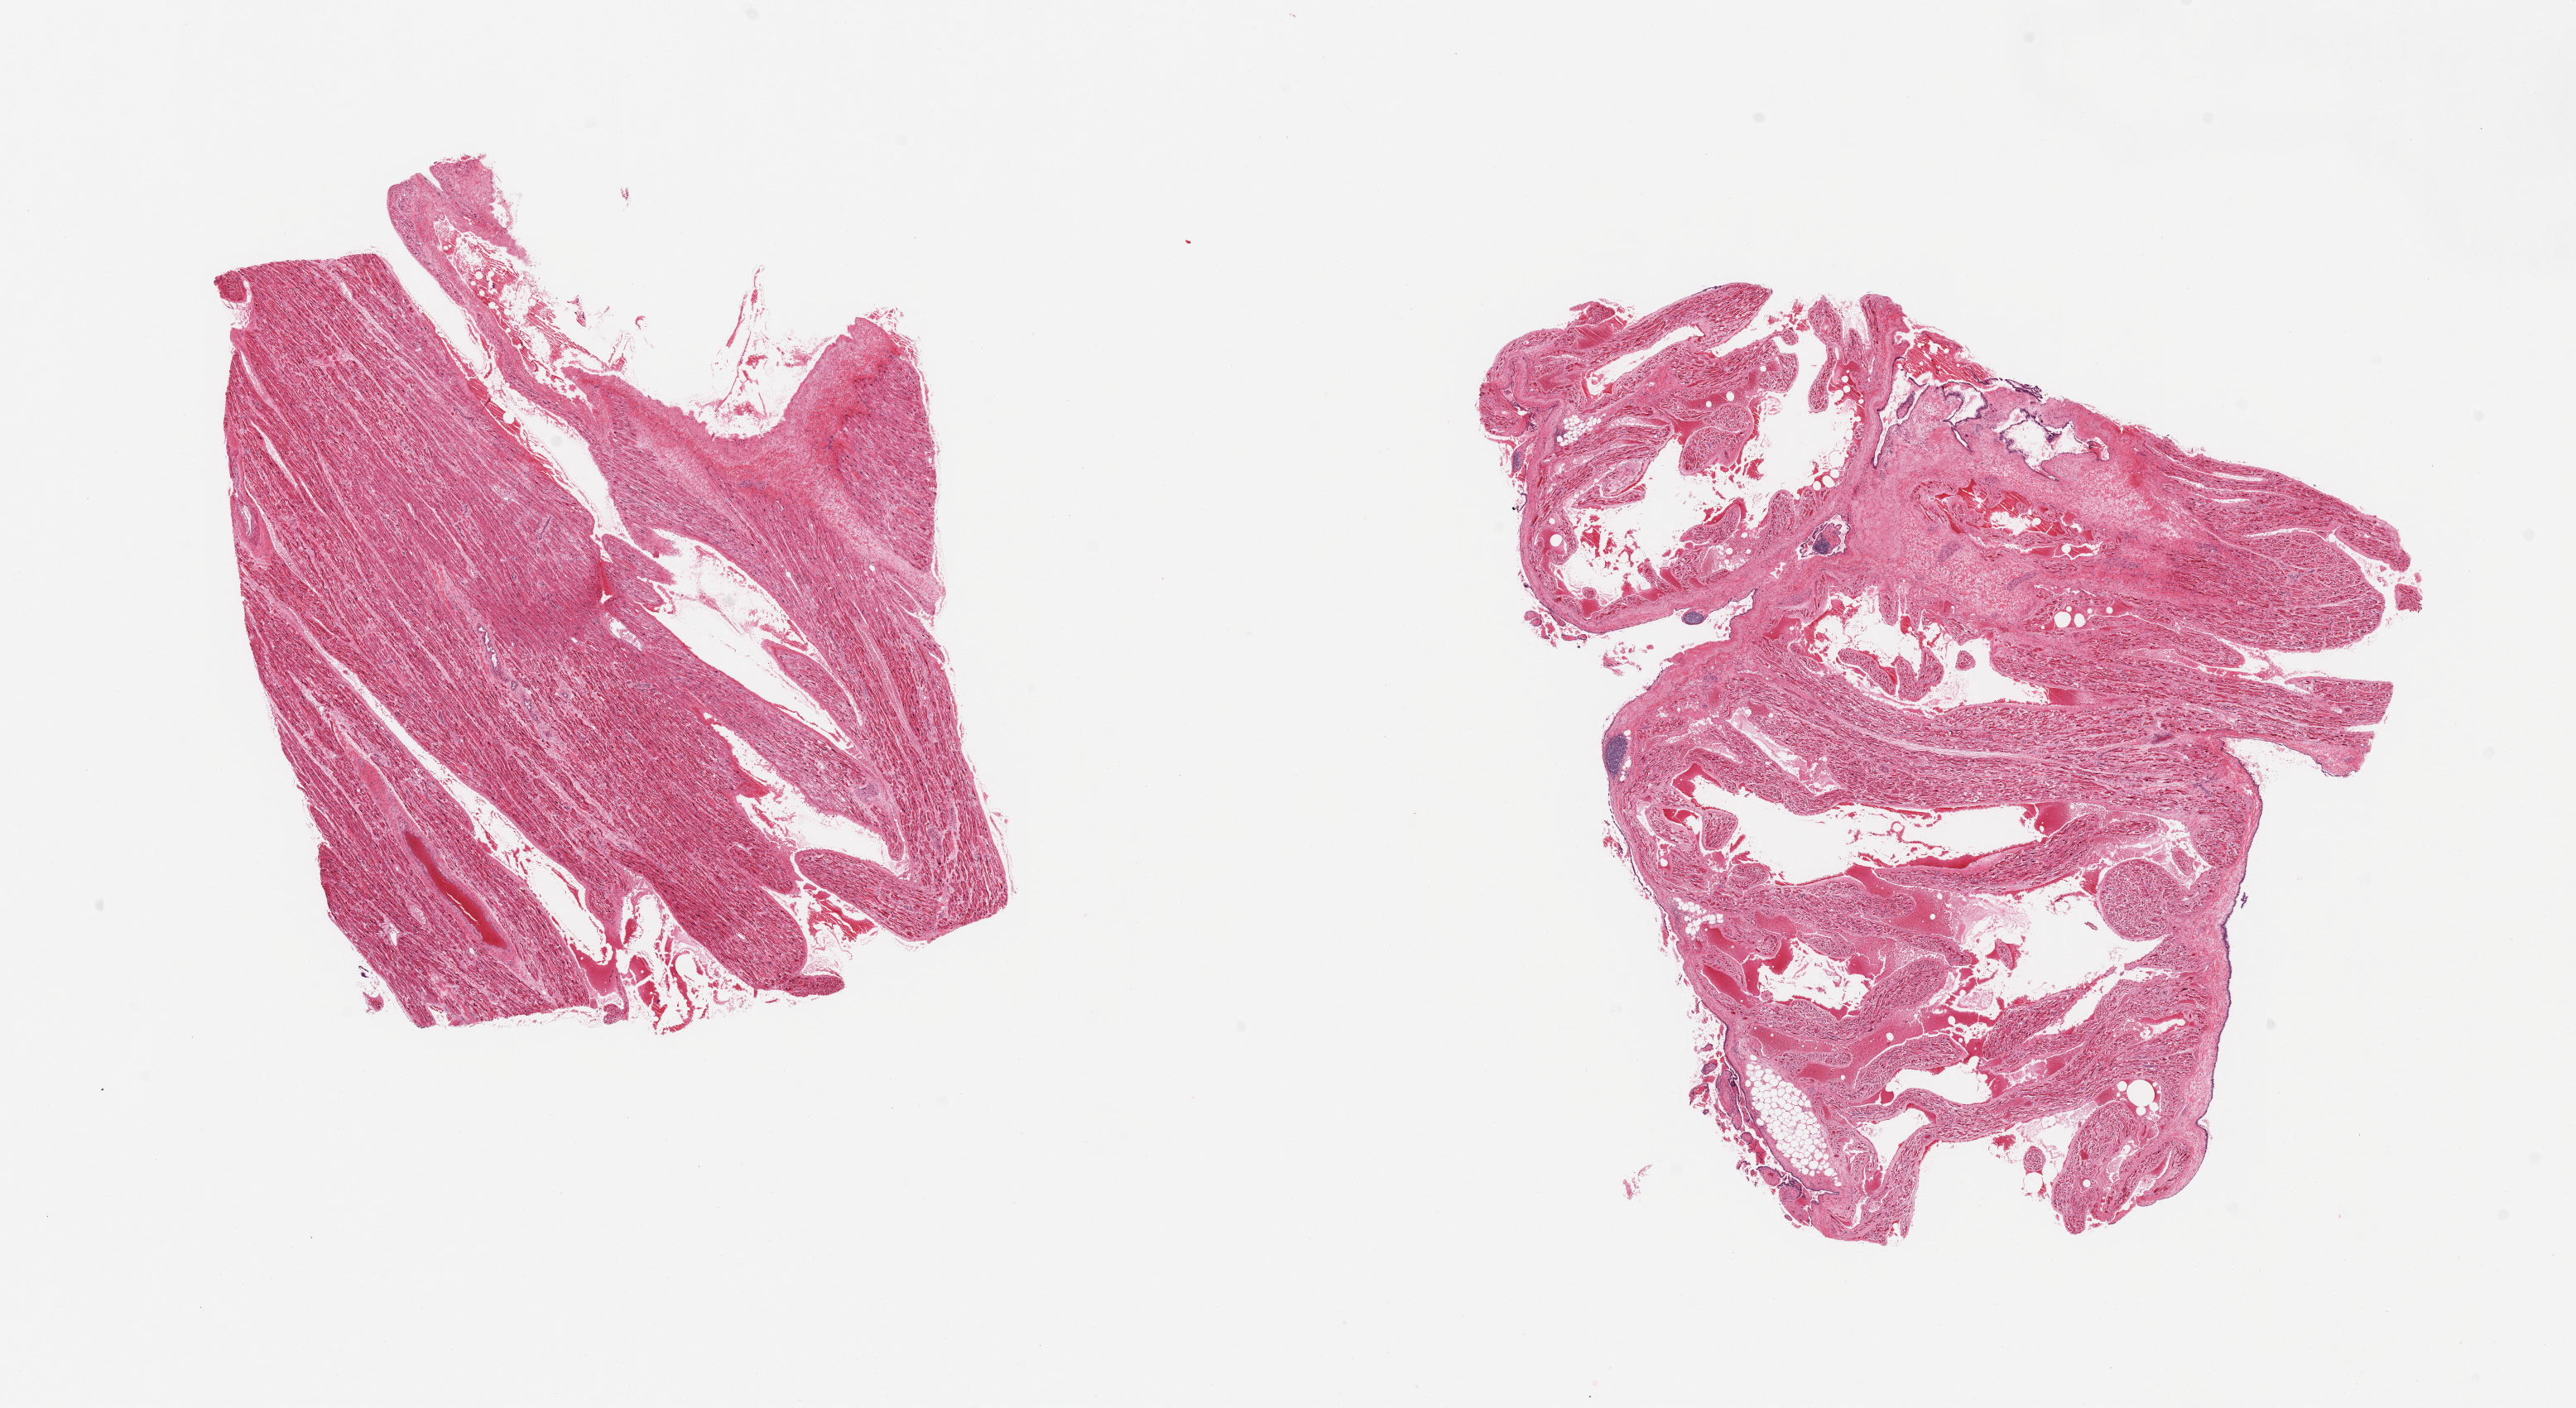
Haematoxylin and eosin whole-slide image — whole scanned area (about 24.6 x 13.5 mm, acquisition: 20x scan) shown as a low-resolution overview, PAXgene-fixed, paraffin-embedded tissue, section of auricular appendage (target tissue), tissue donor sample. Male donor.
* pathologist's review note for this sample: 2 pieces; 10% internal fat; scattered small aggregates of lymphocytes (oulined)